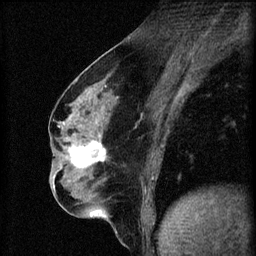
Breast MRI (dynamic contrast-enhanced), one sagittal slice. Slice 29 of 60 in the series (ordered by position). 3 images stored at this slice position (order not interpretable as contrast timing). 1.5 T. TE 4.2 ms, TR 8.2 ms. 2 mm slice thickness. 256 × 256 image matrix, field of view 180 × 180 mm. Female patient, age 56 years.
Annotated regions visible in this slice (semi-automatic segmentation, software-assisted and operator-edited):
- analysis volume of interest (the breast-tissue region the enhancement analysis was run in; not a lesion): bounding box [x1, y1, x2, y2] px = [62, 136, 109, 179]
- tumour enhancement mask (voxels above the 70 % enhancement threshold inside the analysis volume of interest): [68, 136, 105, 169]